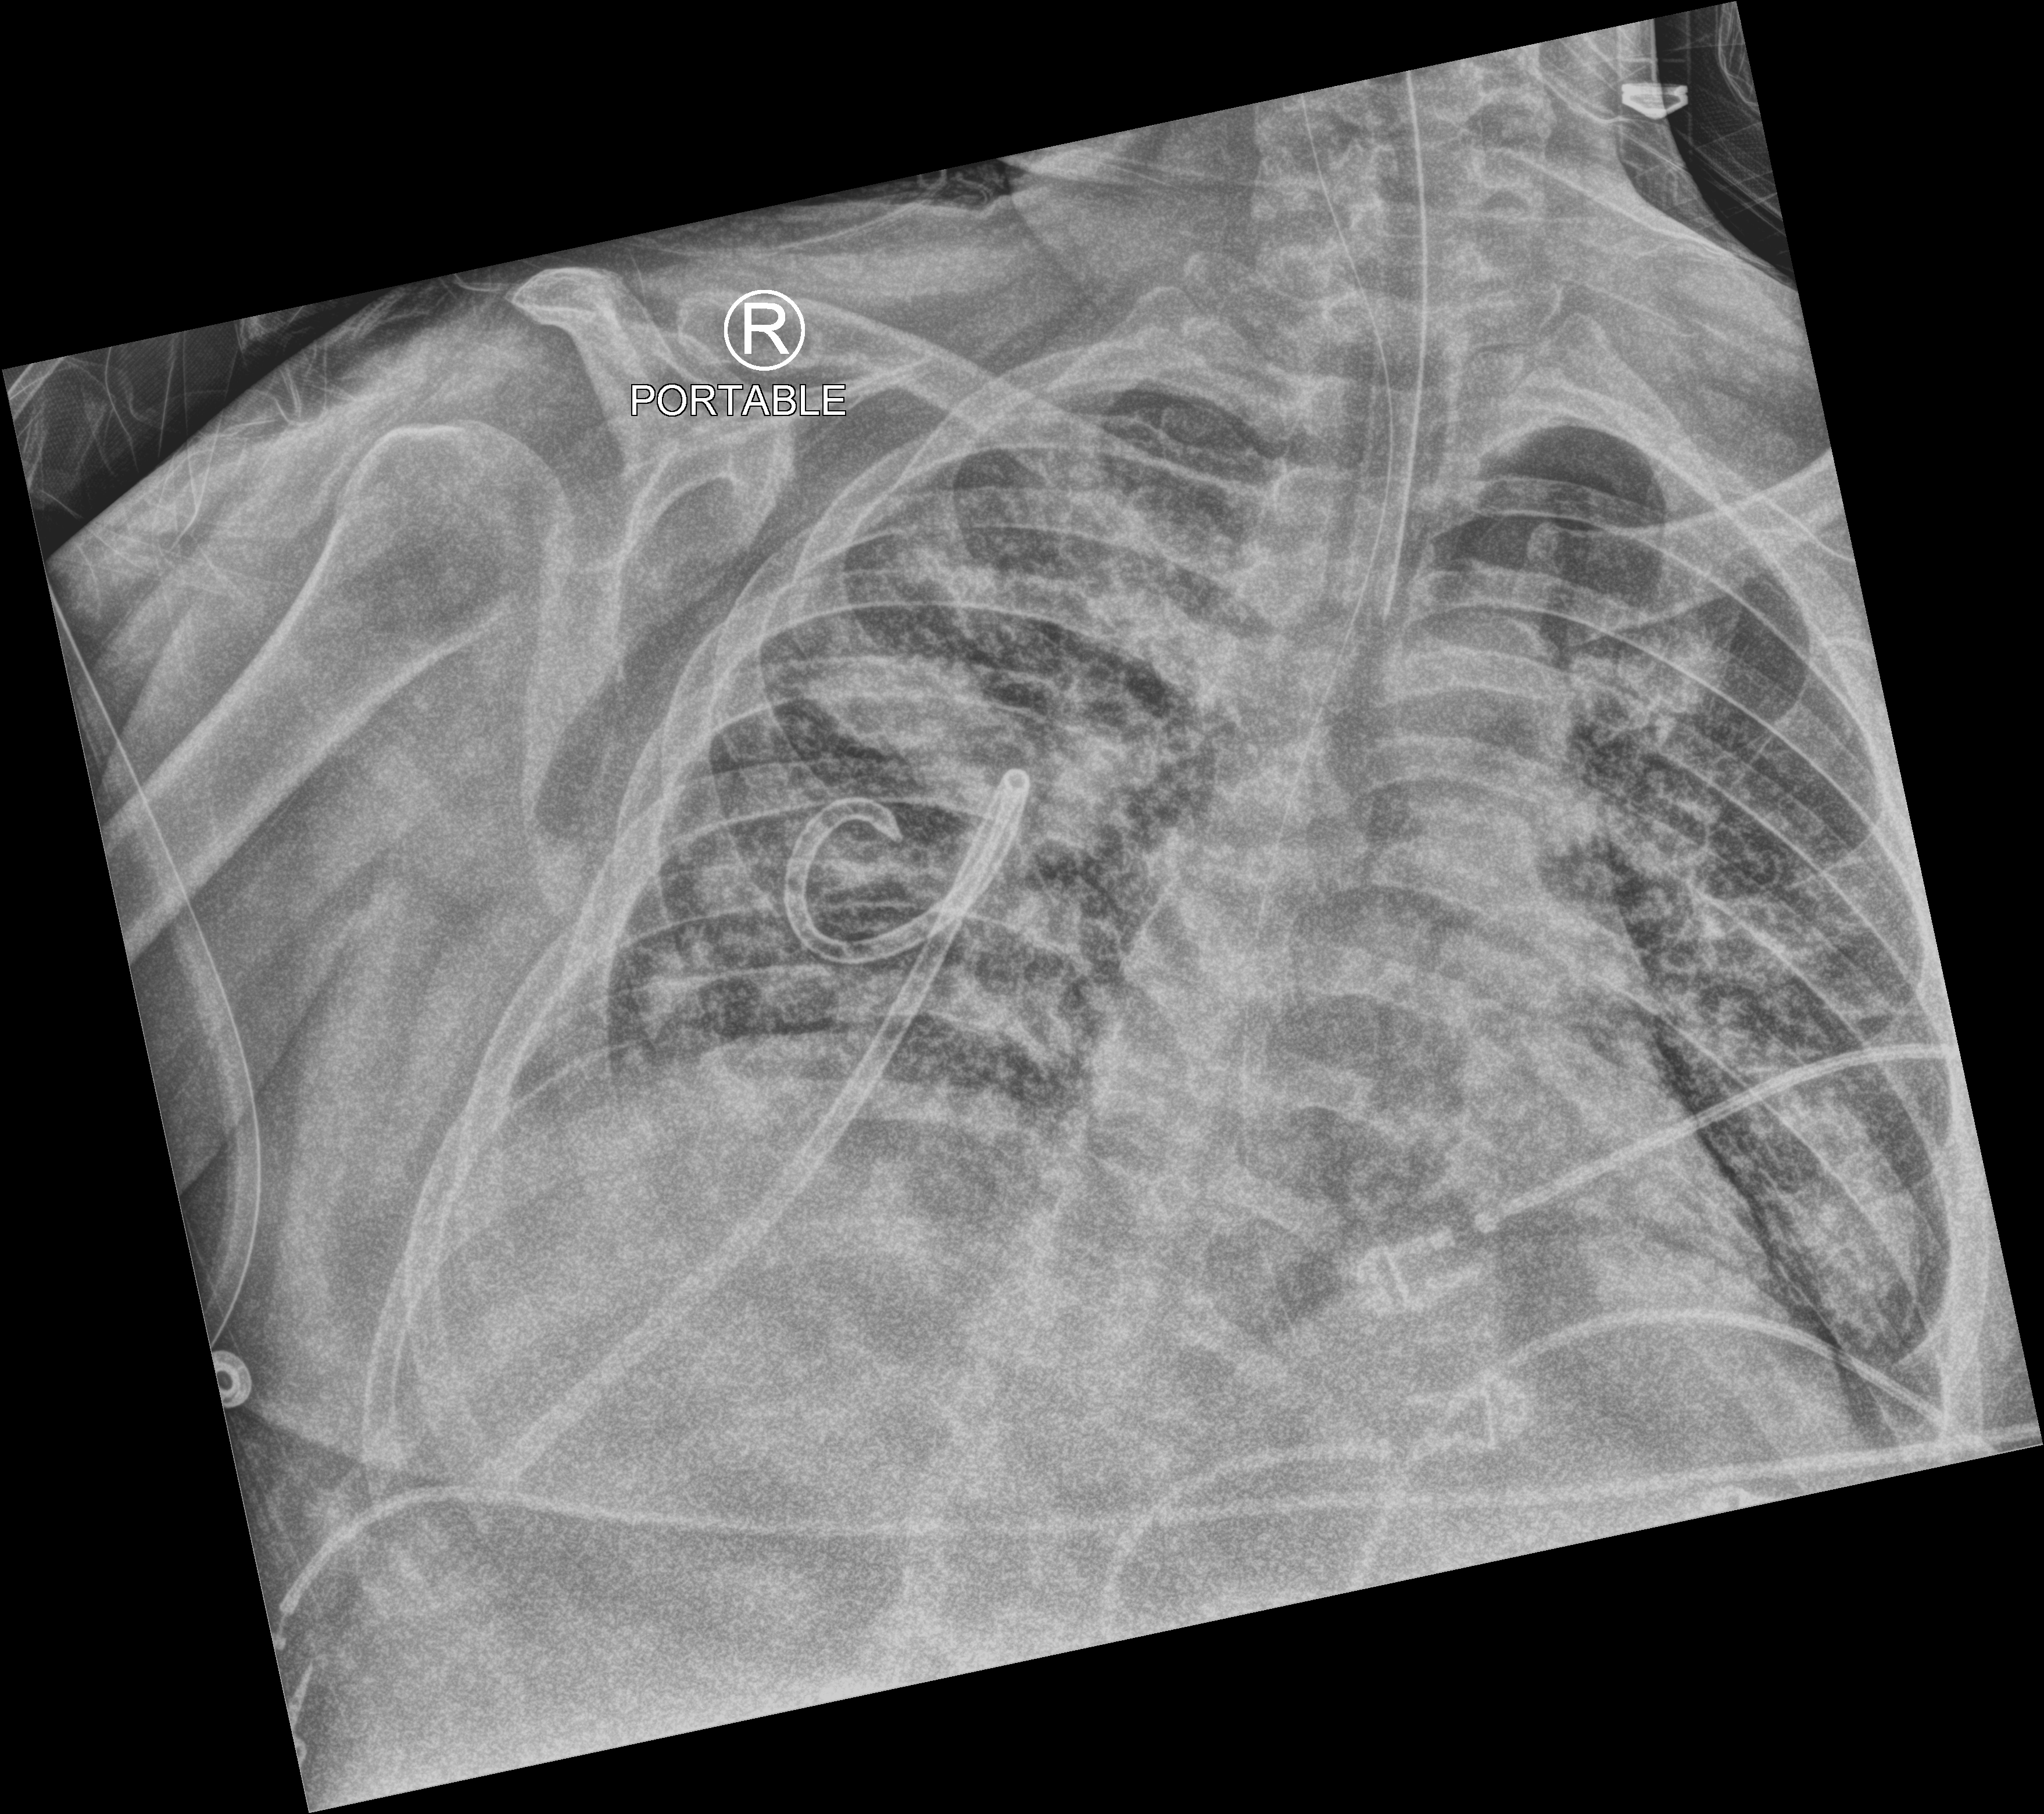
Chest X-ray (portable), anteroposterior (AP) projection. Patient hospitalised with COVID-19, aged 18–59 years.
From the hospital-stay record, not from the radiograph (when in the stay this image was taken is not recorded): mechanically ventilated during this hospital stay: yes; length of hospital stay: 31 days.